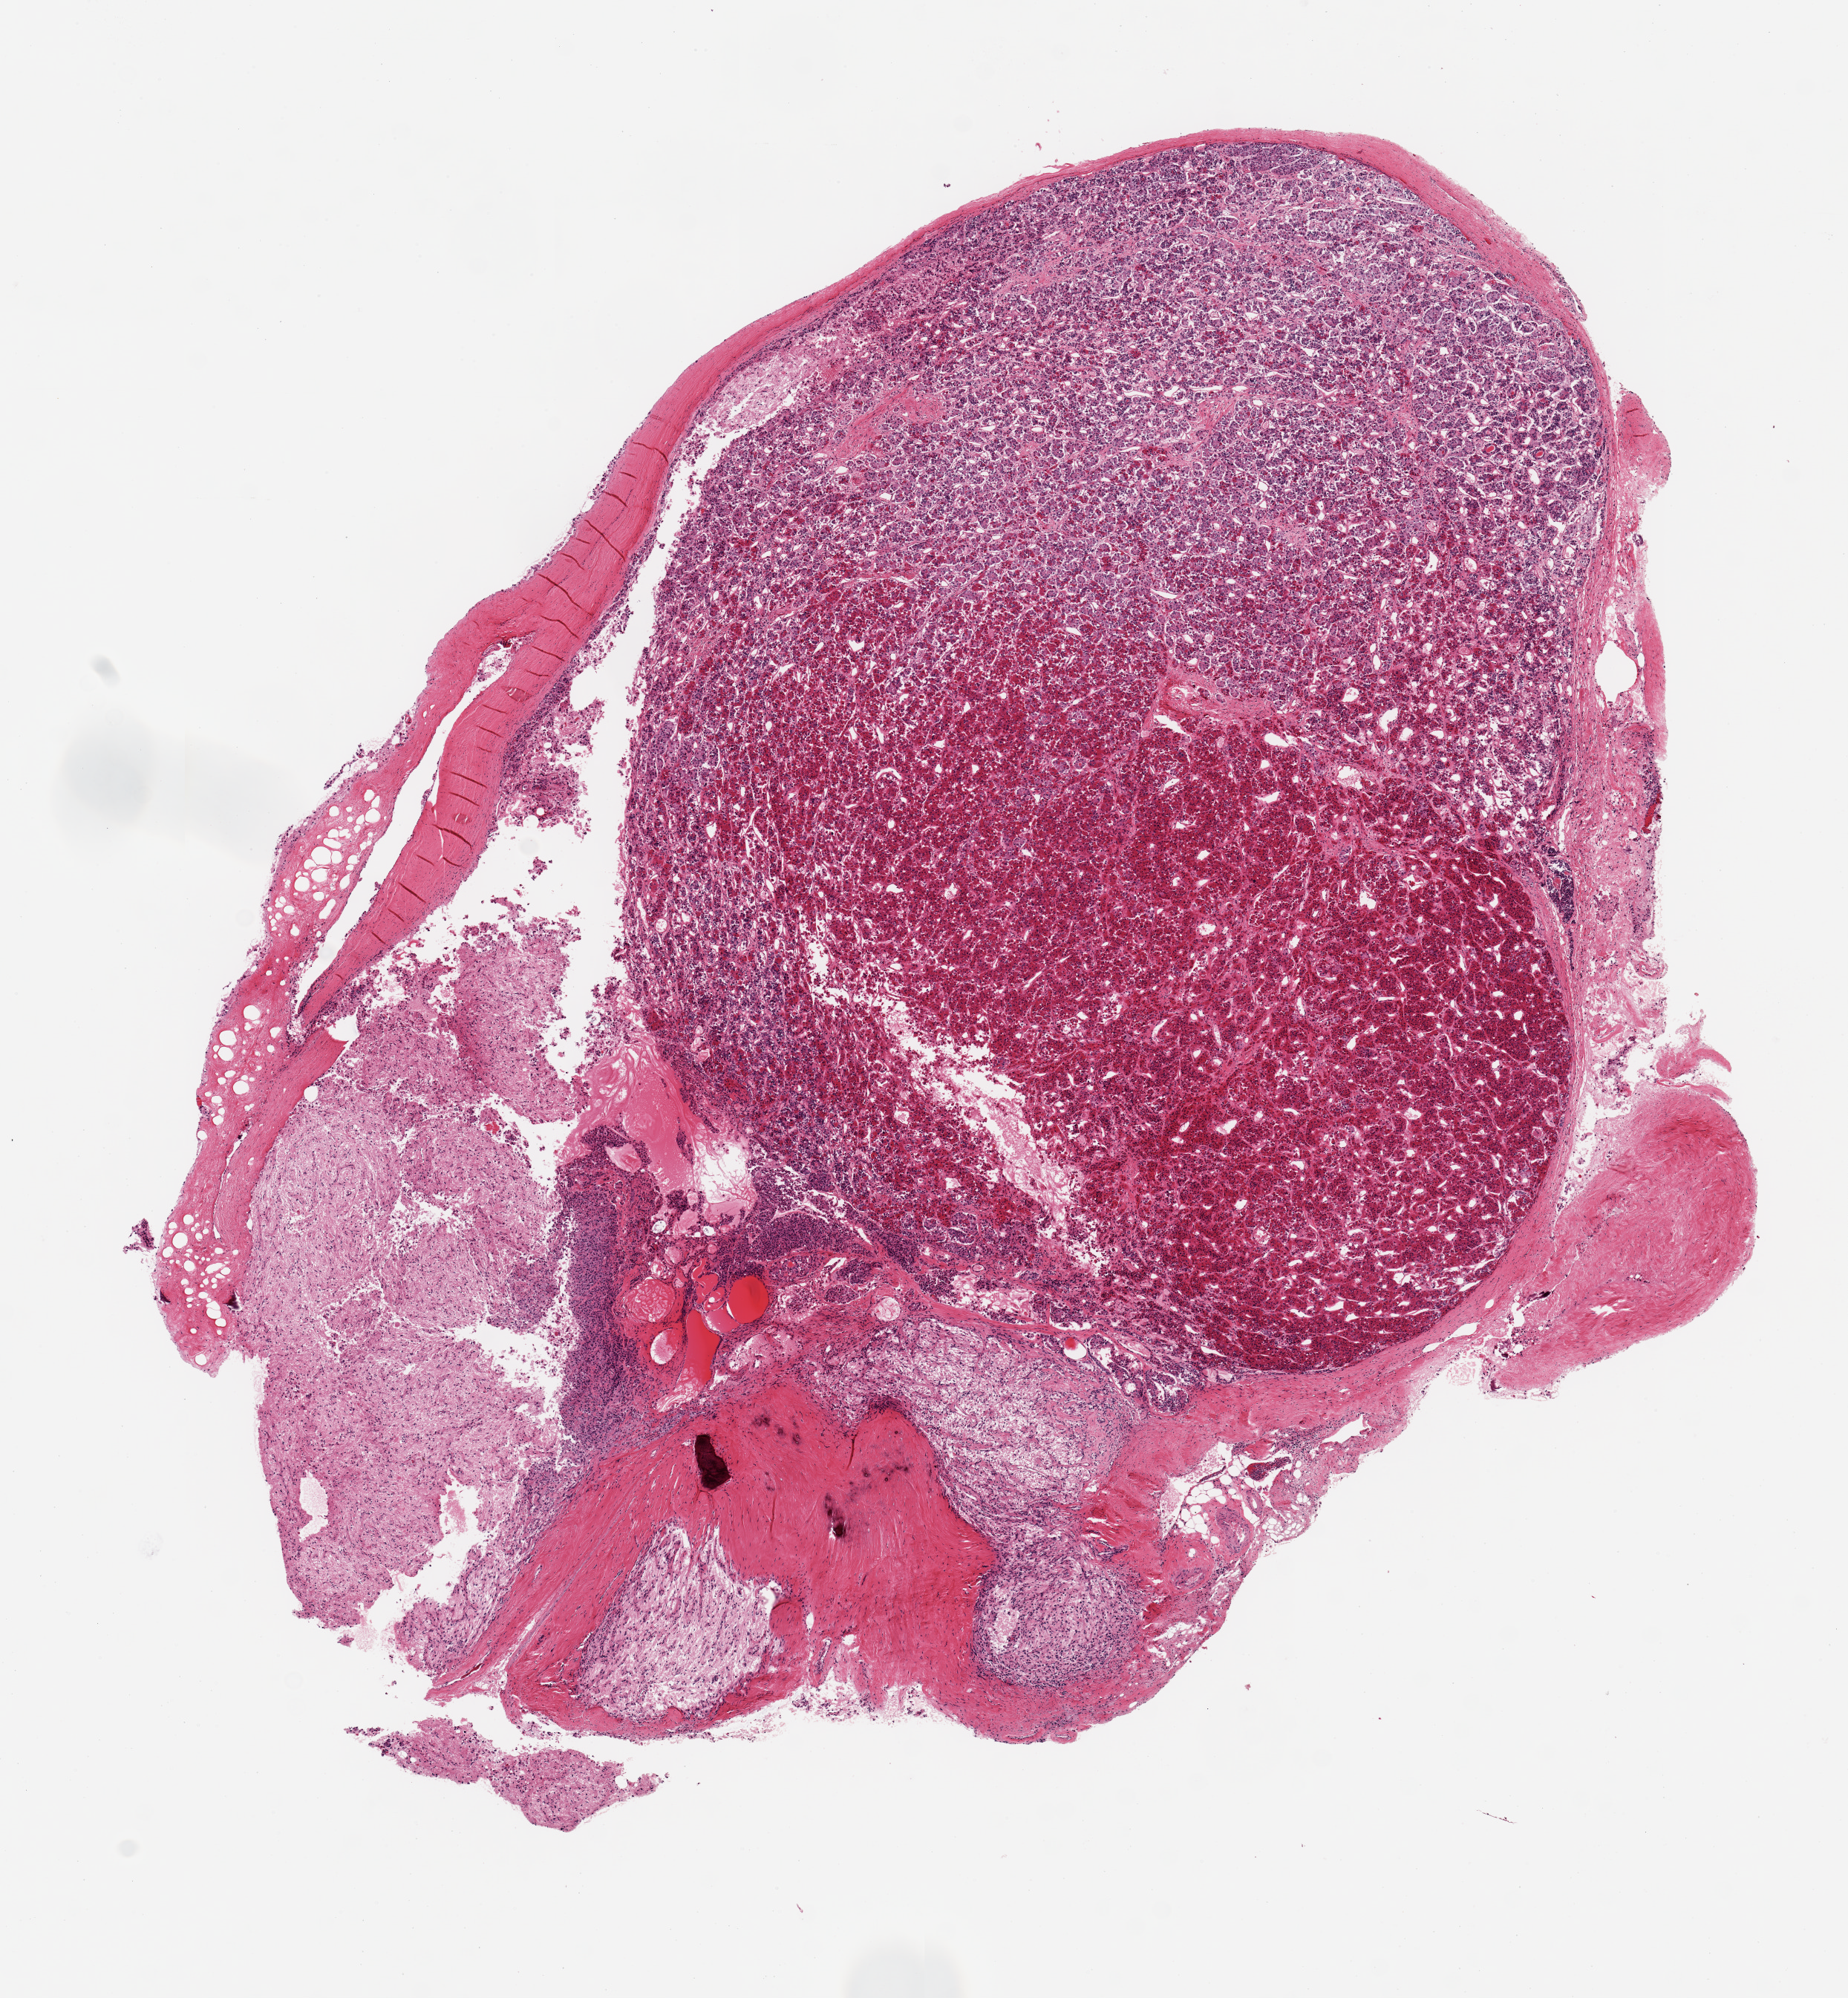
Whole-slide image, haematoxylin and eosin stain, low-resolution overview of the scanned area, about 9.8 x 10.6 mm (slide scanned at 20x). PAXgene-fixed, paraffin-embedded tissue. Section of pituitary (target tissue). Tissue donor sample. Male donor.
Pathologist's review note for this sample: 1 ~8x6mm aliquot. Nice example with both adenohypophysis (6x6mm) and neurohypophysis (~5x2mm).